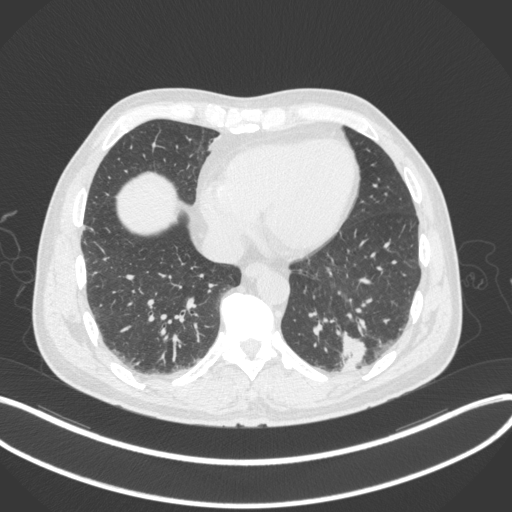
Chest CT, one axial slice; position 86 of 313 along the scan axis; lung window (W 1500 / L -600 HU); 512 × 512 image matrix, field of view 400 × 400 mm. Patient: male, 54 years. From the clinical record (not read from this slice): clinical TNM (as recorded): T1c N0 M1; histopathological grade: G3.
Structures marked on this image (rectangle marked by the reading radiologist):
- lung tumour (recorded histology: adenocarcinoma): bounding box <335,329,372,375> (left, top, right, bottom; pixels)